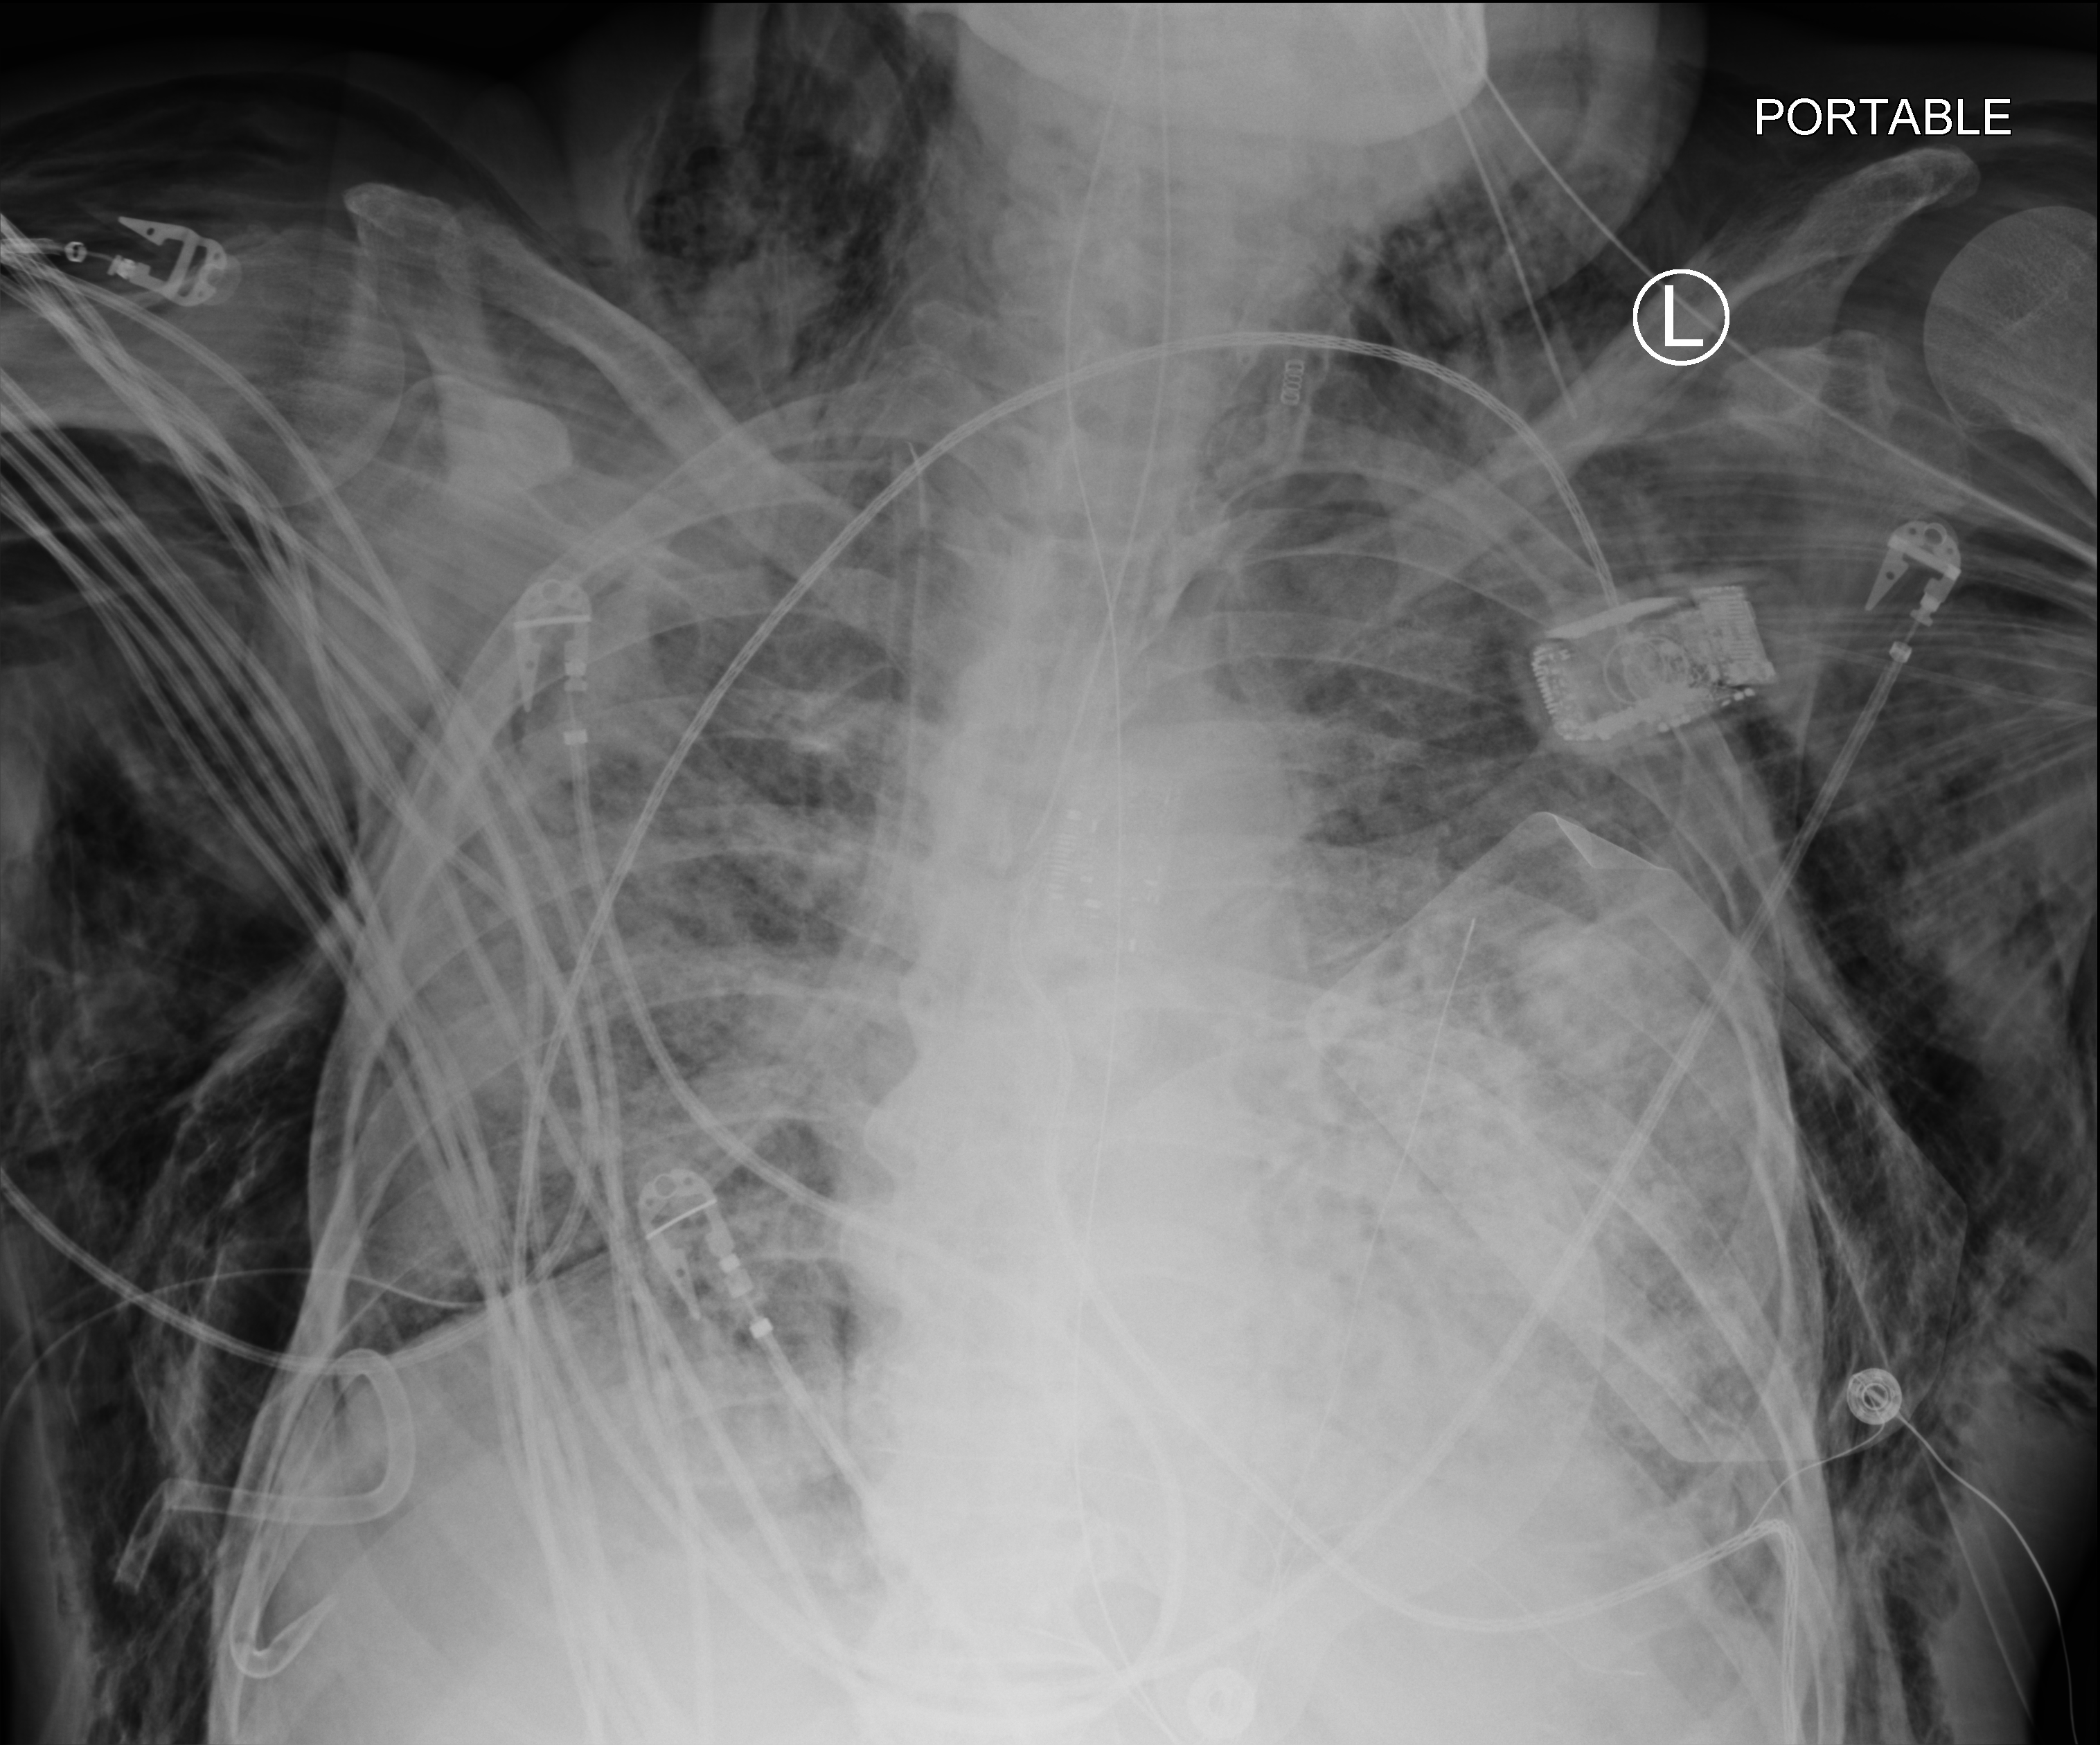
Chest X-ray (portable), anteroposterior (AP) projection. Male patient hospitalised with COVID-19, age 75–90 years.
Hospital-stay facts (about this admission, not read from this image; timing relative to this image not recorded): admitted to intensive care during this hospital stay: yes.